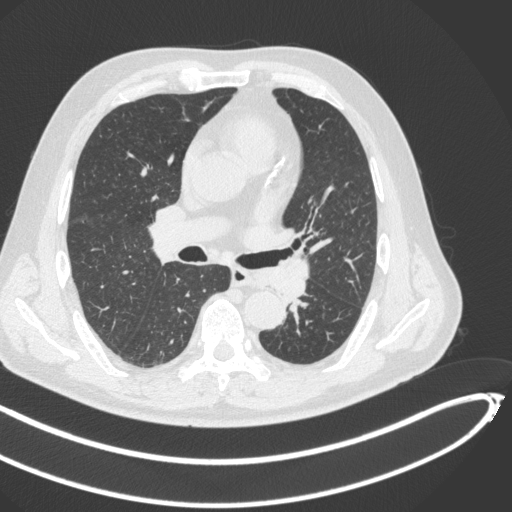
Chest CT, one axial slice. Slice 263 of 466 in the series (ordered by position). Reconstruction kernel B31f. 120 kVp. Lung window (W 1500 / L -600 HU). 1 mm slice thickness. 512 × 512 image matrix. Patient: male, 64 years. From the clinical record (not read from this slice): clinical TNM (as recorded): T1c N0 M0.
Outlined on this slice (rectangle marked by the reading radiologist):
- lung tumour (recorded histology: squamous cell carcinoma): bounding box [x1, y1, x2, y2] px = [254, 260, 311, 303]